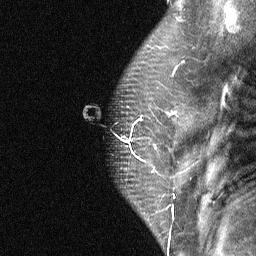
Breast MRI (dynamic contrast-enhanced), one sagittal slice. Position 51 of 64 along the scan axis. Dynamic contrast-enhanced study with each time point stored as its own series, time point 2 of 4 at this slice position (early post-contrast, ordered by acquisition time). 1.5 T. TE 4.8 ms, TR 27 ms. 256 × 256 image matrix, field of view 180 × 180 mm. Patient: female, 50 years. Case-level facts recorded for this patient, not image findings: setting: breast cancer imaged before/during neoadjuvant chemotherapy; receptor status: HER2-positive.
Outlined on this slice (semi-automatically segmented with operator editing):
- analysis volume of interest (the breast-tissue region the enhancement analysis was run in; not a lesion): bounding box <123,91,189,177> (left, top, right, bottom; pixels)
- tumour enhancement mask (voxels above the 90 % enhancement threshold inside the analysis volume of interest): <123,112,174,143>